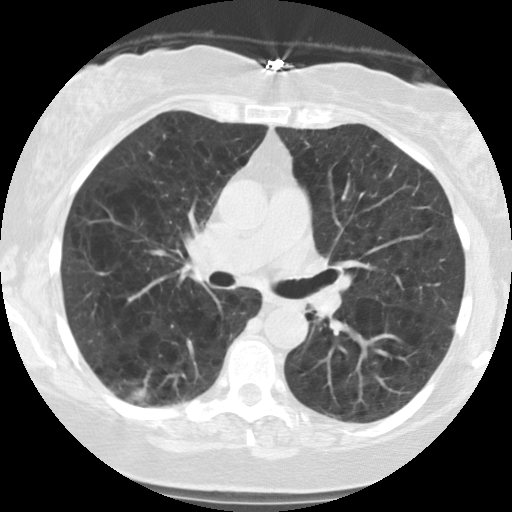
Chest CT (low-dose screening protocol), one axial image. Second annual screen. Lung window (W 1500 / L -600 HU). Slice 55 of 122 in the series. Female, age 59 years at enrolment. Current smoker at enrolment.
Lesion marked by an expert reader, bounding box [x1, y1, x2, y2] px = [105, 358, 173, 418]. The screening reader recorded 2 non-calcified nodules or masses ≥4 mm on this exam (right lower lobe, right lower lobe); which of them this box marks is not recorded. Official screen result: positive, other.